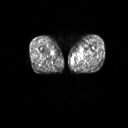
FDG PET of an extremity soft-tissue mass (from a PET/CT study), one axial slice; position 10 of 267 along the scan axis; 128 × 128 image matrix, field of view 600 × 600 mm. Patient: male, 59 years. From the clinical record (not read from this slice): histological type: pleiomorphic liposarcoma; grade: high; site of the primary tumour: left thigh.
Outlined on this slice (expert contour drawn on MRI and transferred to this co-registered scan by the dataset authors):
- gross tumour volume including surrounding oedema: bounding box <78,52,87,59> (left, top, right, bottom; pixels)